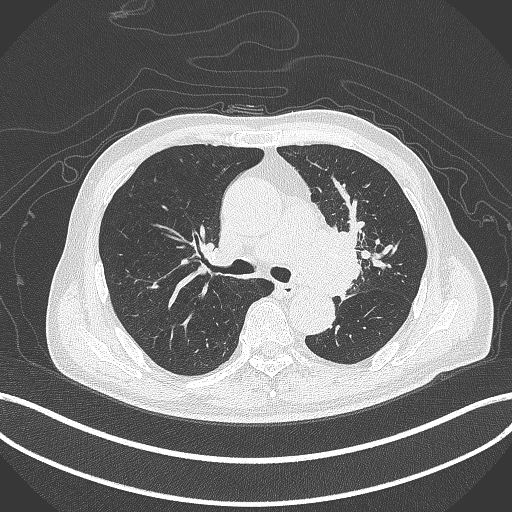
Chest CT, one axial slice. Slice 273 of 417 in the series (ordered by position). Reconstruction kernel B70f. Lung window (W 1500 / L -600 HU). 1 mm slice thickness. 512 × 512 image matrix, field of view 400 × 400 mm. Male patient, age 77 years. From the clinical record (not read from this slice): clinical TNM (as recorded): T3 N1 M0.
Outlined on this slice (bounding box drawn by a radiologist):
- lung tumour (recorded histology: adenocarcinoma): box from (x=315, y=219) to (x=368, y=298) px